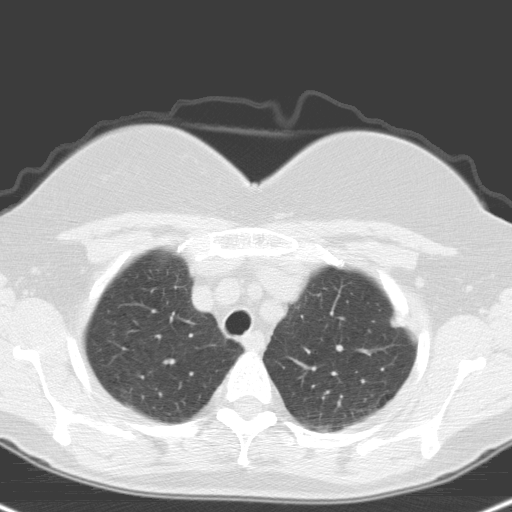
Low-dose screening chest CT, one axial slice; slice 128 of 148 in the series (ordered by position); lung window (W 1500 / L -600 HU); 512 × 512 image matrix, field of view 314 × 314 mm.
Structures marked on this image (expert manual segmentation):
- lesion 1 (tumor, upper lobe of left lung): bounding box [x1, y1, x2, y2] px = [390, 316, 402, 328]